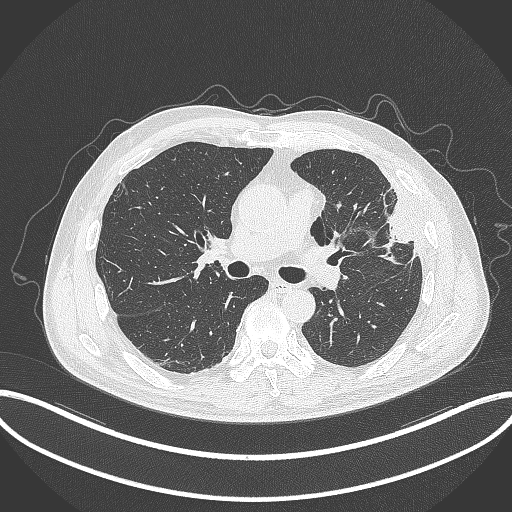
Chest CT, one axial slice; slice 197 of 382 in the series (ordered by position); 120 kVp; lung window (W 1500 / L -600 HU); 512 × 512 image matrix. Patient: male, 64 years. From the clinical record (not read from this slice): clinical TNM (as recorded): T4 N1 M0.
Outlined on this slice (bounding box drawn by a radiologist):
- lung tumour (recorded histology: adenocarcinoma): bounding box <365,186,416,262> (left, top, right, bottom; pixels)